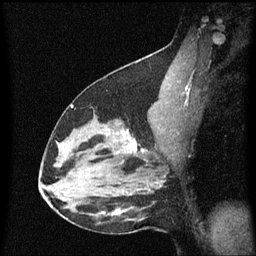
Breast MRI (dynamic contrast-enhanced), one sagittal slice; position 37 of 60 along the scan axis; dynamic contrast-enhanced series, image 2 of 3 at this slice position (ordered by acquisition); 1.5 T; TE 4.2 ms, TR 8.4 ms; 2 mm slice thickness; 256 × 256 image matrix, field of view 200 × 200 mm. Patient: female, 38 years. From the clinical record (not read from this slice): setting: breast cancer imaged before/during neoadjuvant chemotherapy; receptor status: HR-positive, HER2-negative.
Annotated regions visible in this slice (semi-automatically segmented with operator editing):
- analysis volume of interest (the breast-tissue region the enhancement analysis was run in; not a lesion): bounding box <122,126,154,163> (left, top, right, bottom; pixels)
- tumour enhancement mask (voxels above the 70 % enhancement threshold inside the analysis volume of interest): <126,132,145,153>